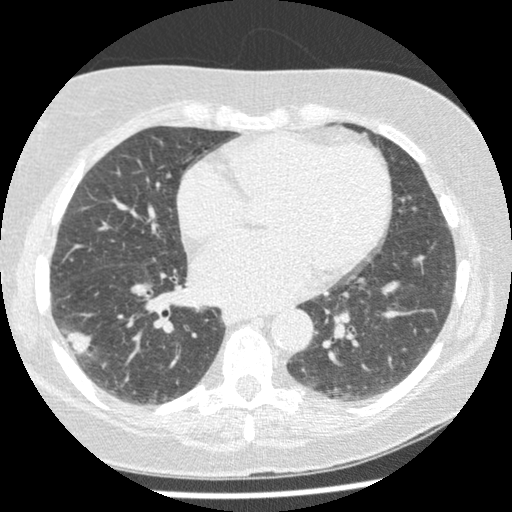
Low-dose screening chest CT, one axial slice; position 105 of 241 along the scan axis; lung window (W 1500 / L -600 HU); 1.25 mm slice thickness; 512 × 512 image matrix, field of view 305 × 305 mm.
Structures marked on this image (outlined manually by an expert reader):
- lesion 1 (tumor, lower lobe of right lung): bounding box <66,330,92,354> (left, top, right, bottom; pixels)